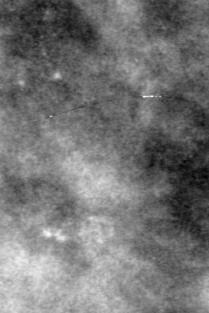
Crop from a digitized film mammogram around one marked abnormality, right breast, MLO view, BI-RADS breast density category 4 (scale 1–4).
- Marked abnormality: calcifications, morphology pleomorphic, distribution clustered; BI-RADS assessment category 4; pathology (as recorded): benign.